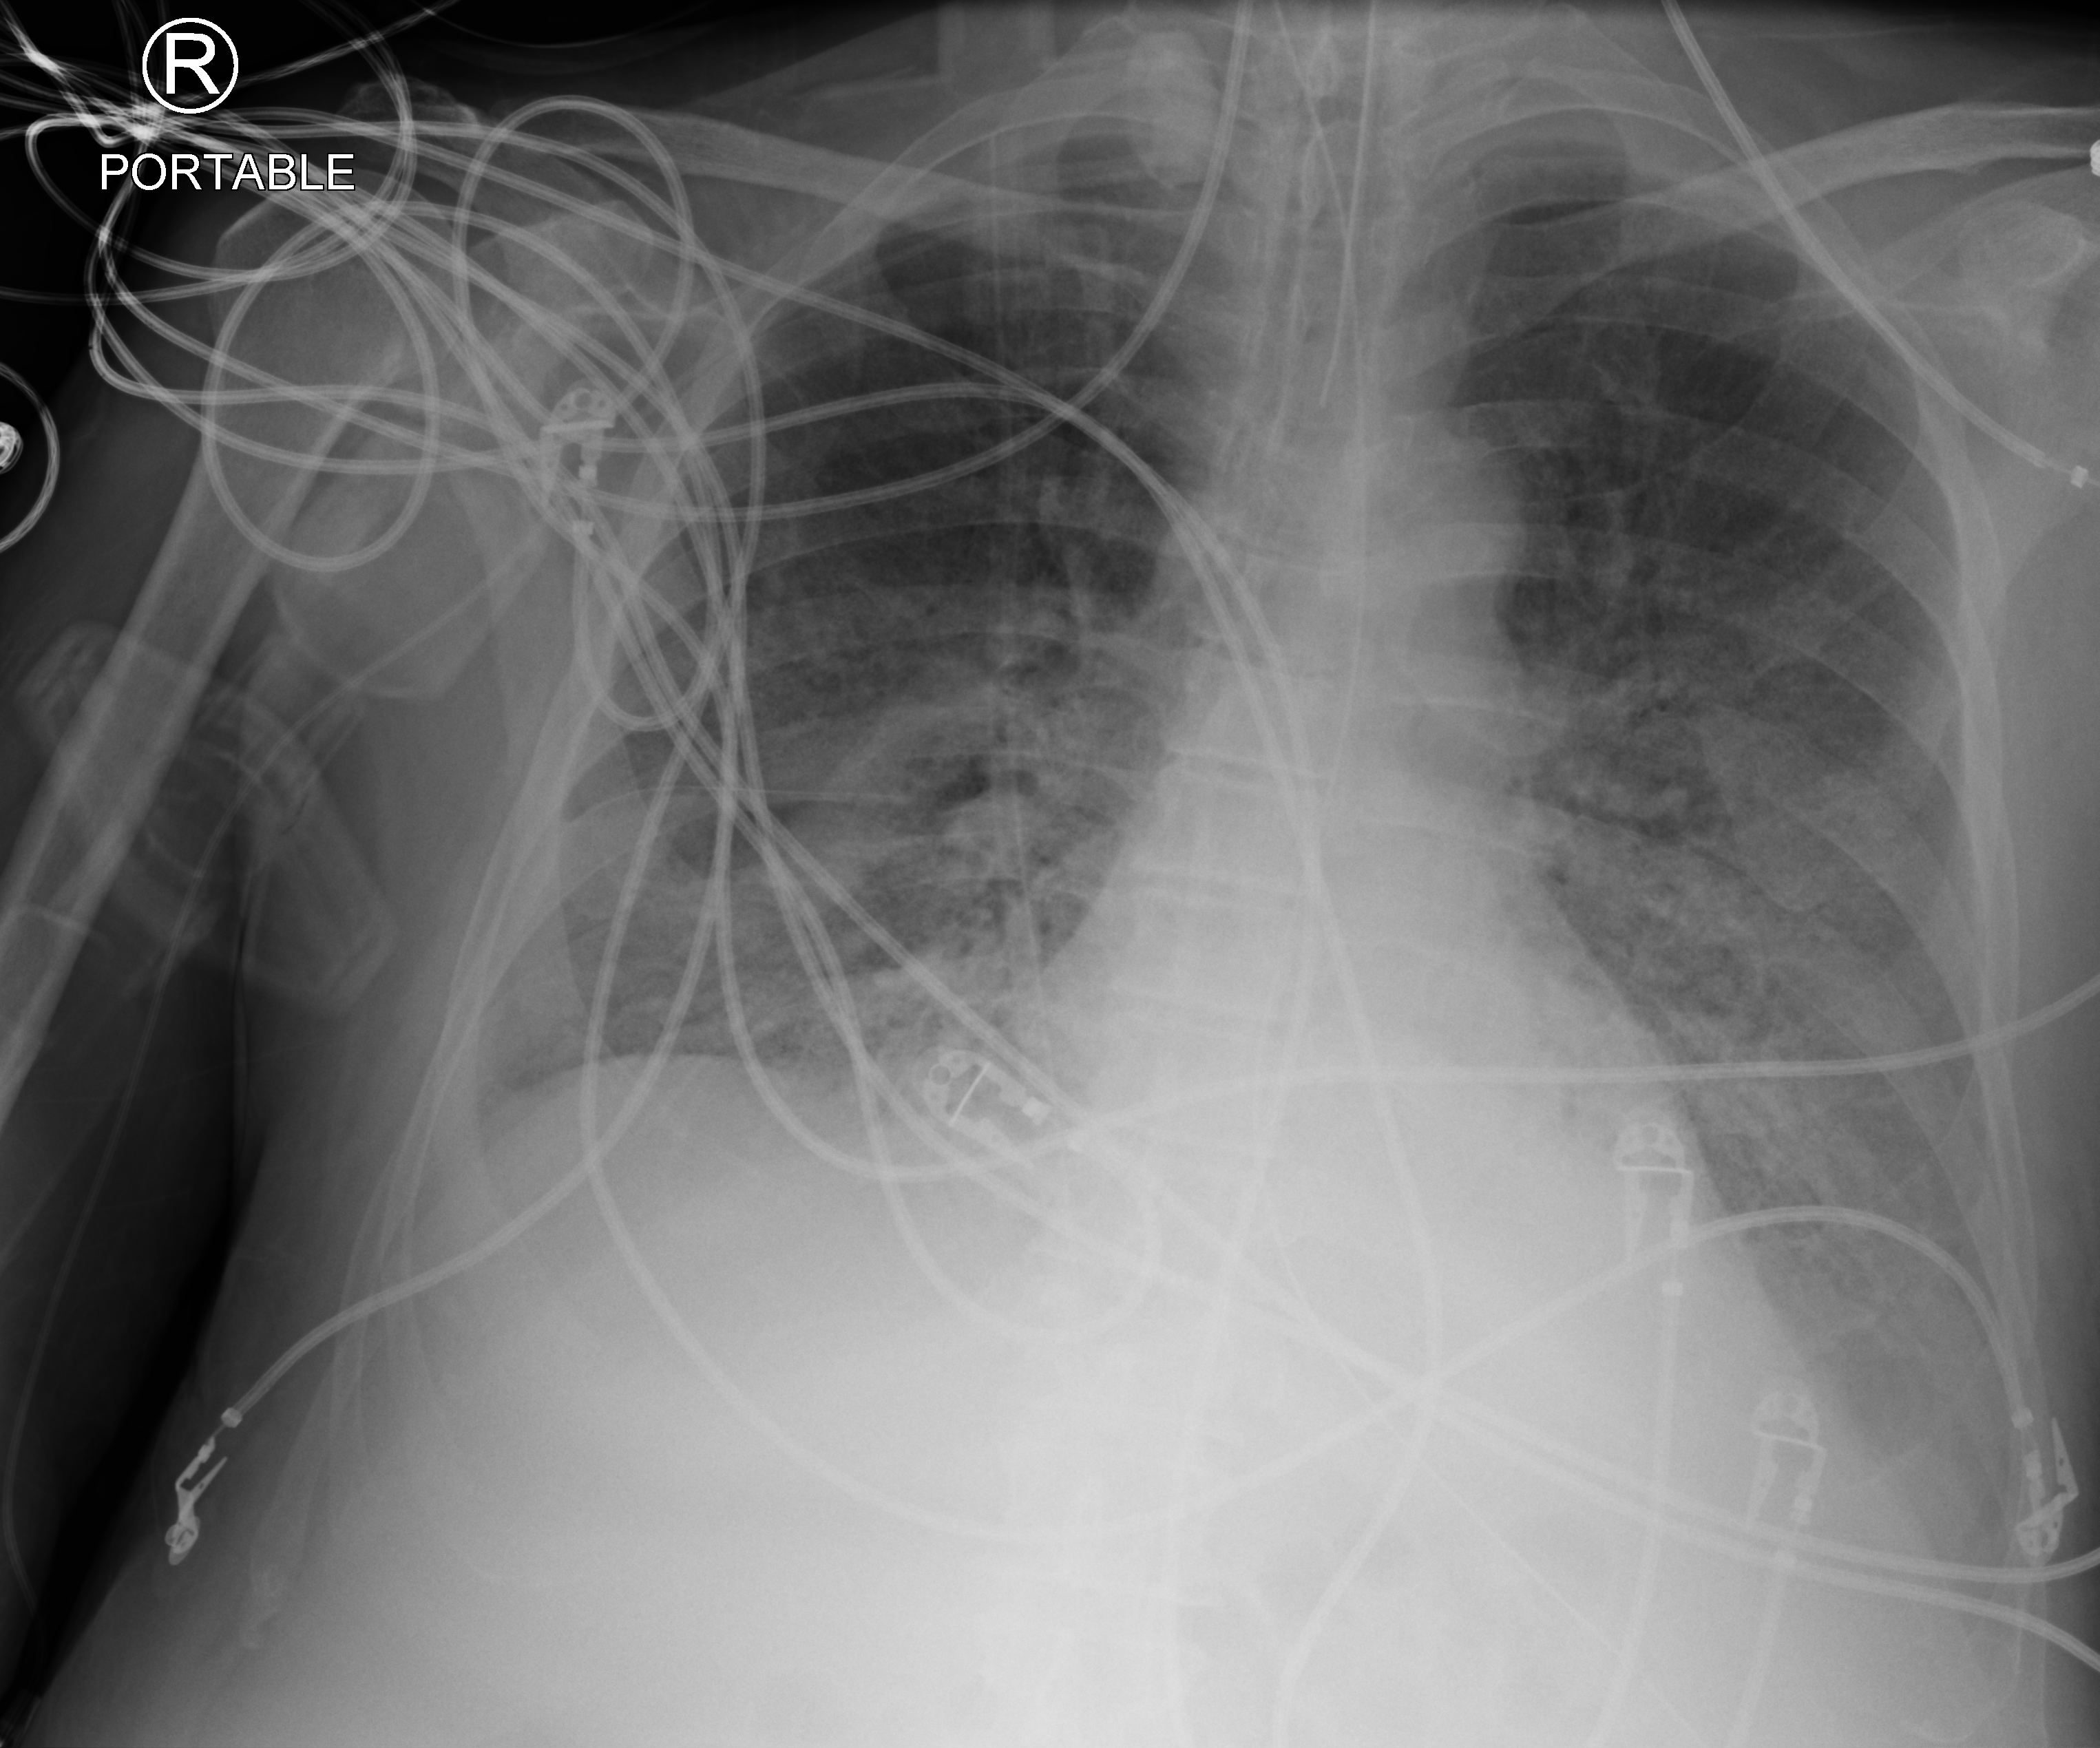
Bedside chest radiograph (computed radiography). Male patient hospitalised with COVID-19, age 60–74 years.
Admission-level facts for this patient (not findings on this image; timing relative to this image not recorded): COPD (admission record): no; admitted to intensive care during this hospital stay: yes; mechanically ventilated during this hospital stay: yes.